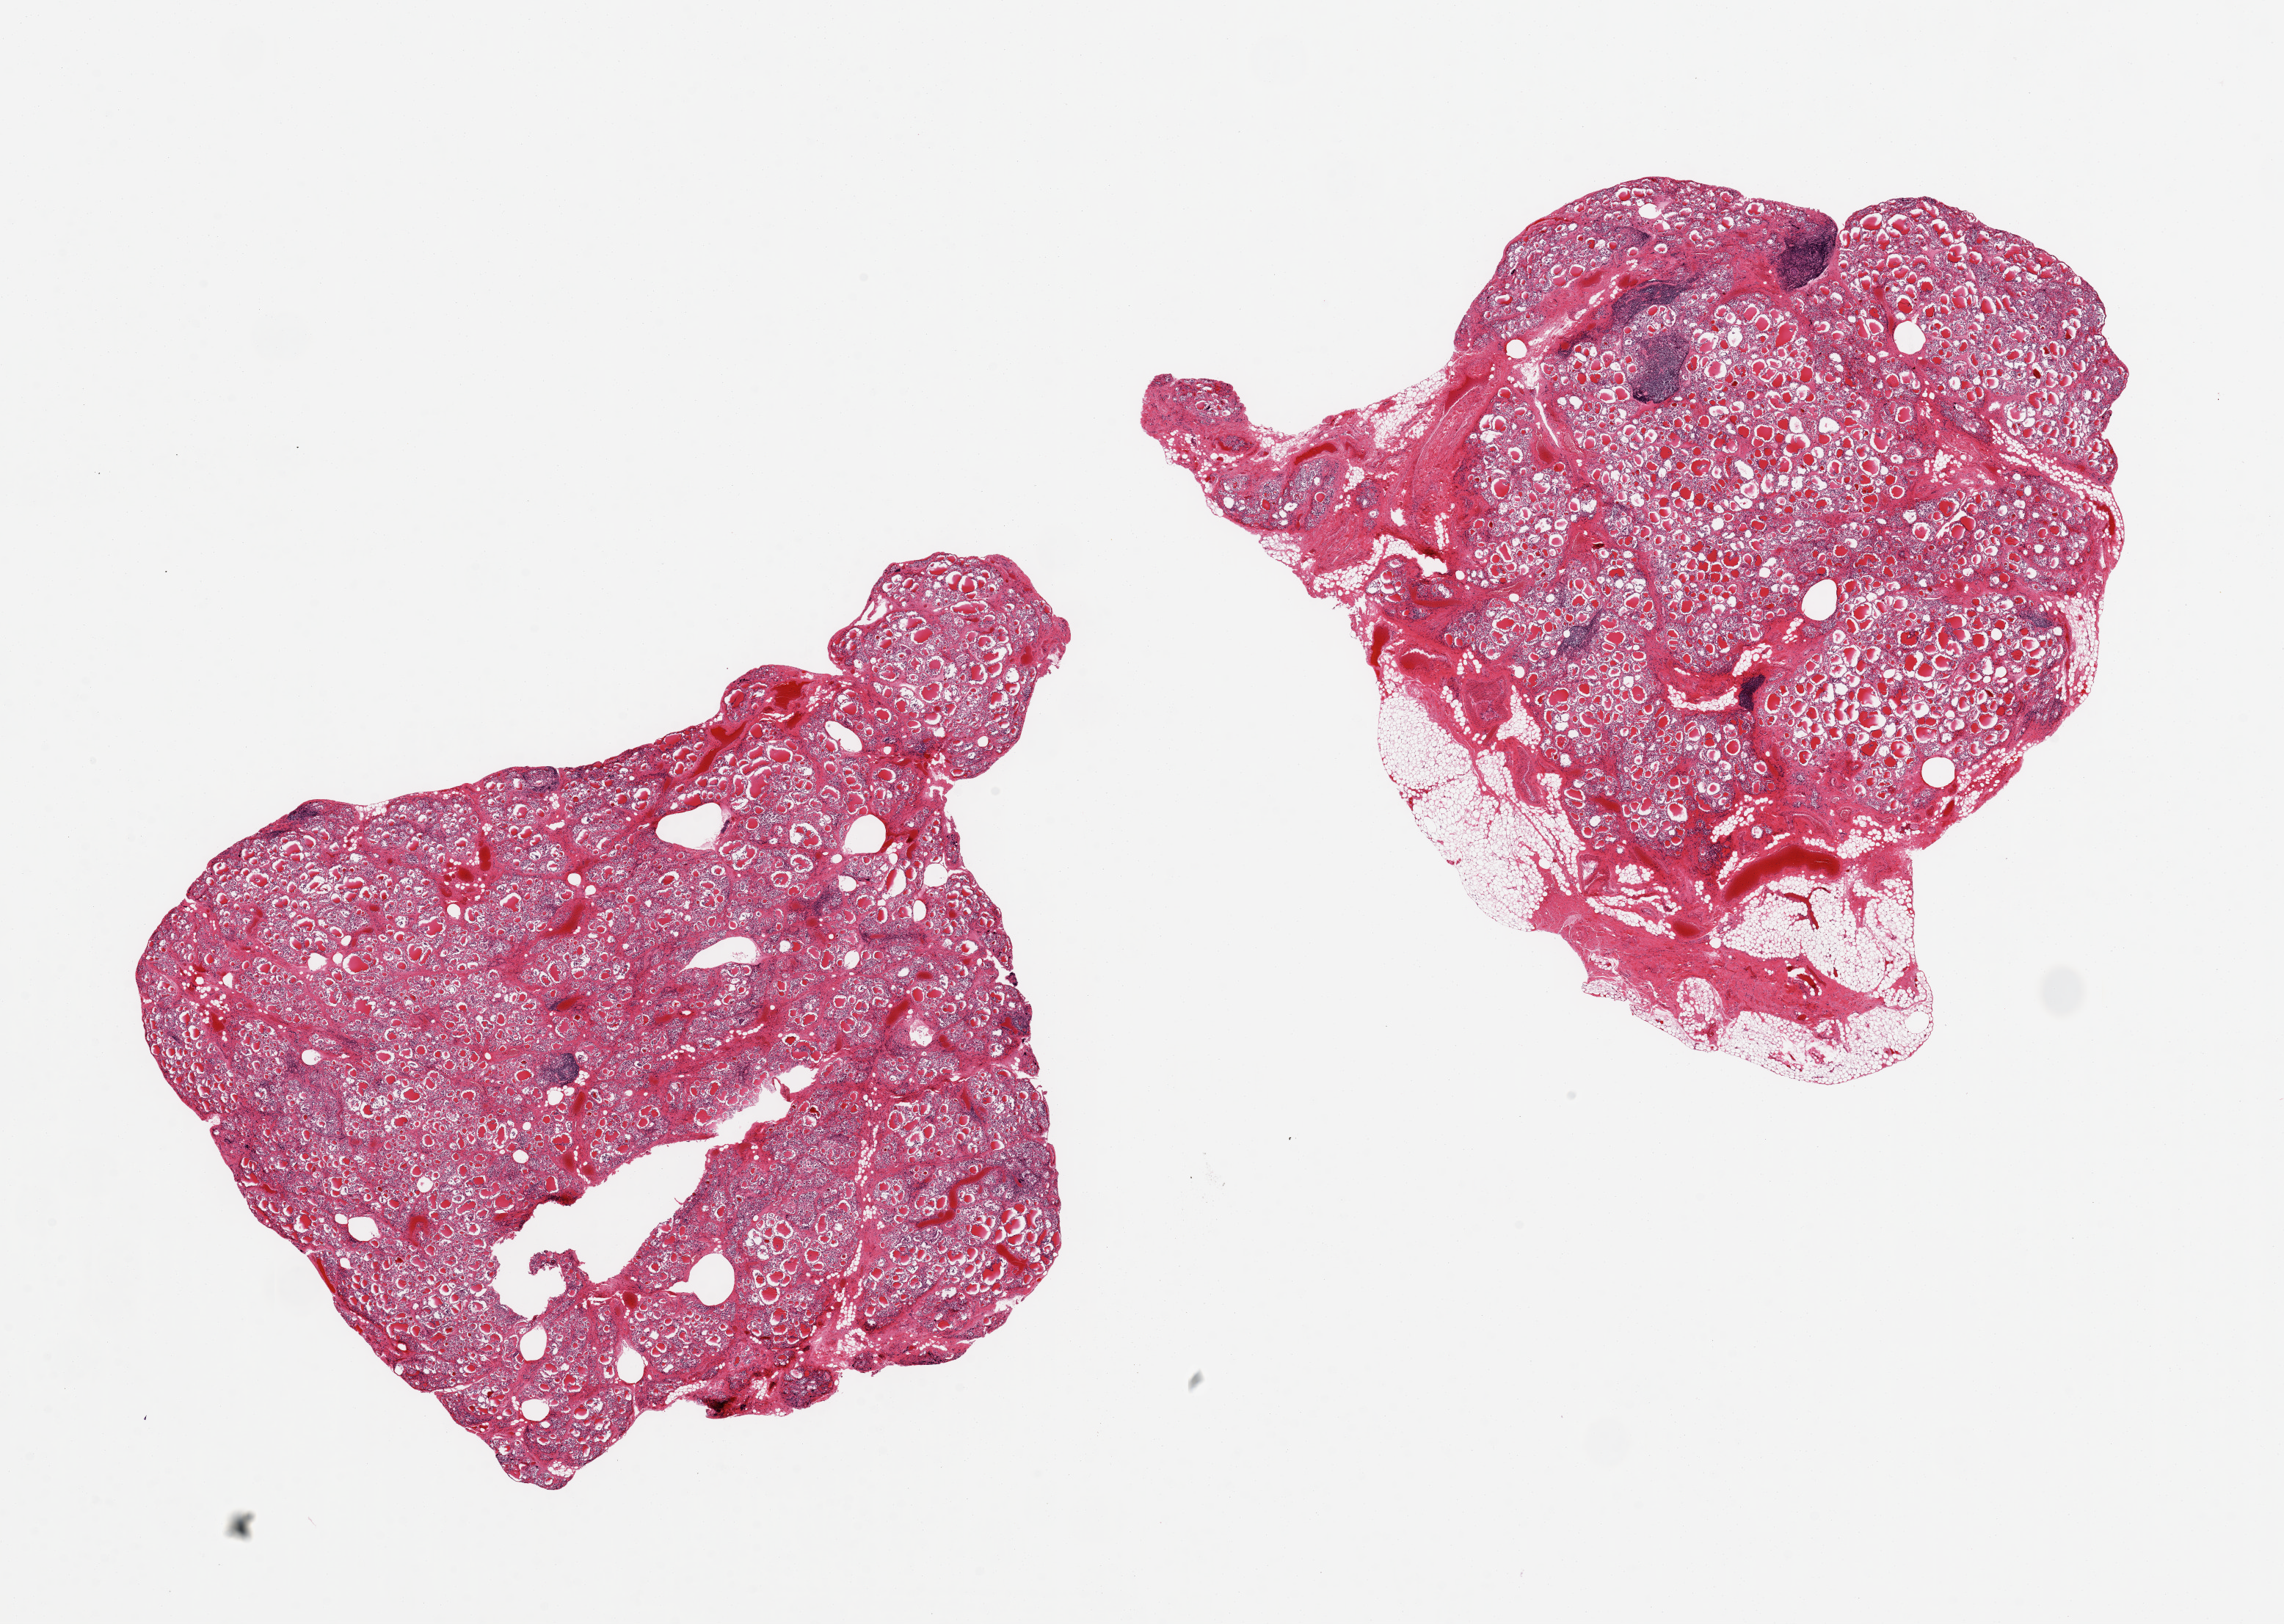
Whole-slide image, hematoxylin and eosin (H&E) stain — a low-resolution overview of the entire scanned area, about 24.6 x 17.5 mm, PAXgene-fixed paraffin-embedded (PFPE) section, sampled site (target tissue): thyroid, tissue donor sample. Male donor.
Reviewer comment on this tissue sample: 2 pieces, 11x7 & 9x8 mm; scattered lymphoid nodules; ~20% adipose on edge of 1 piece.